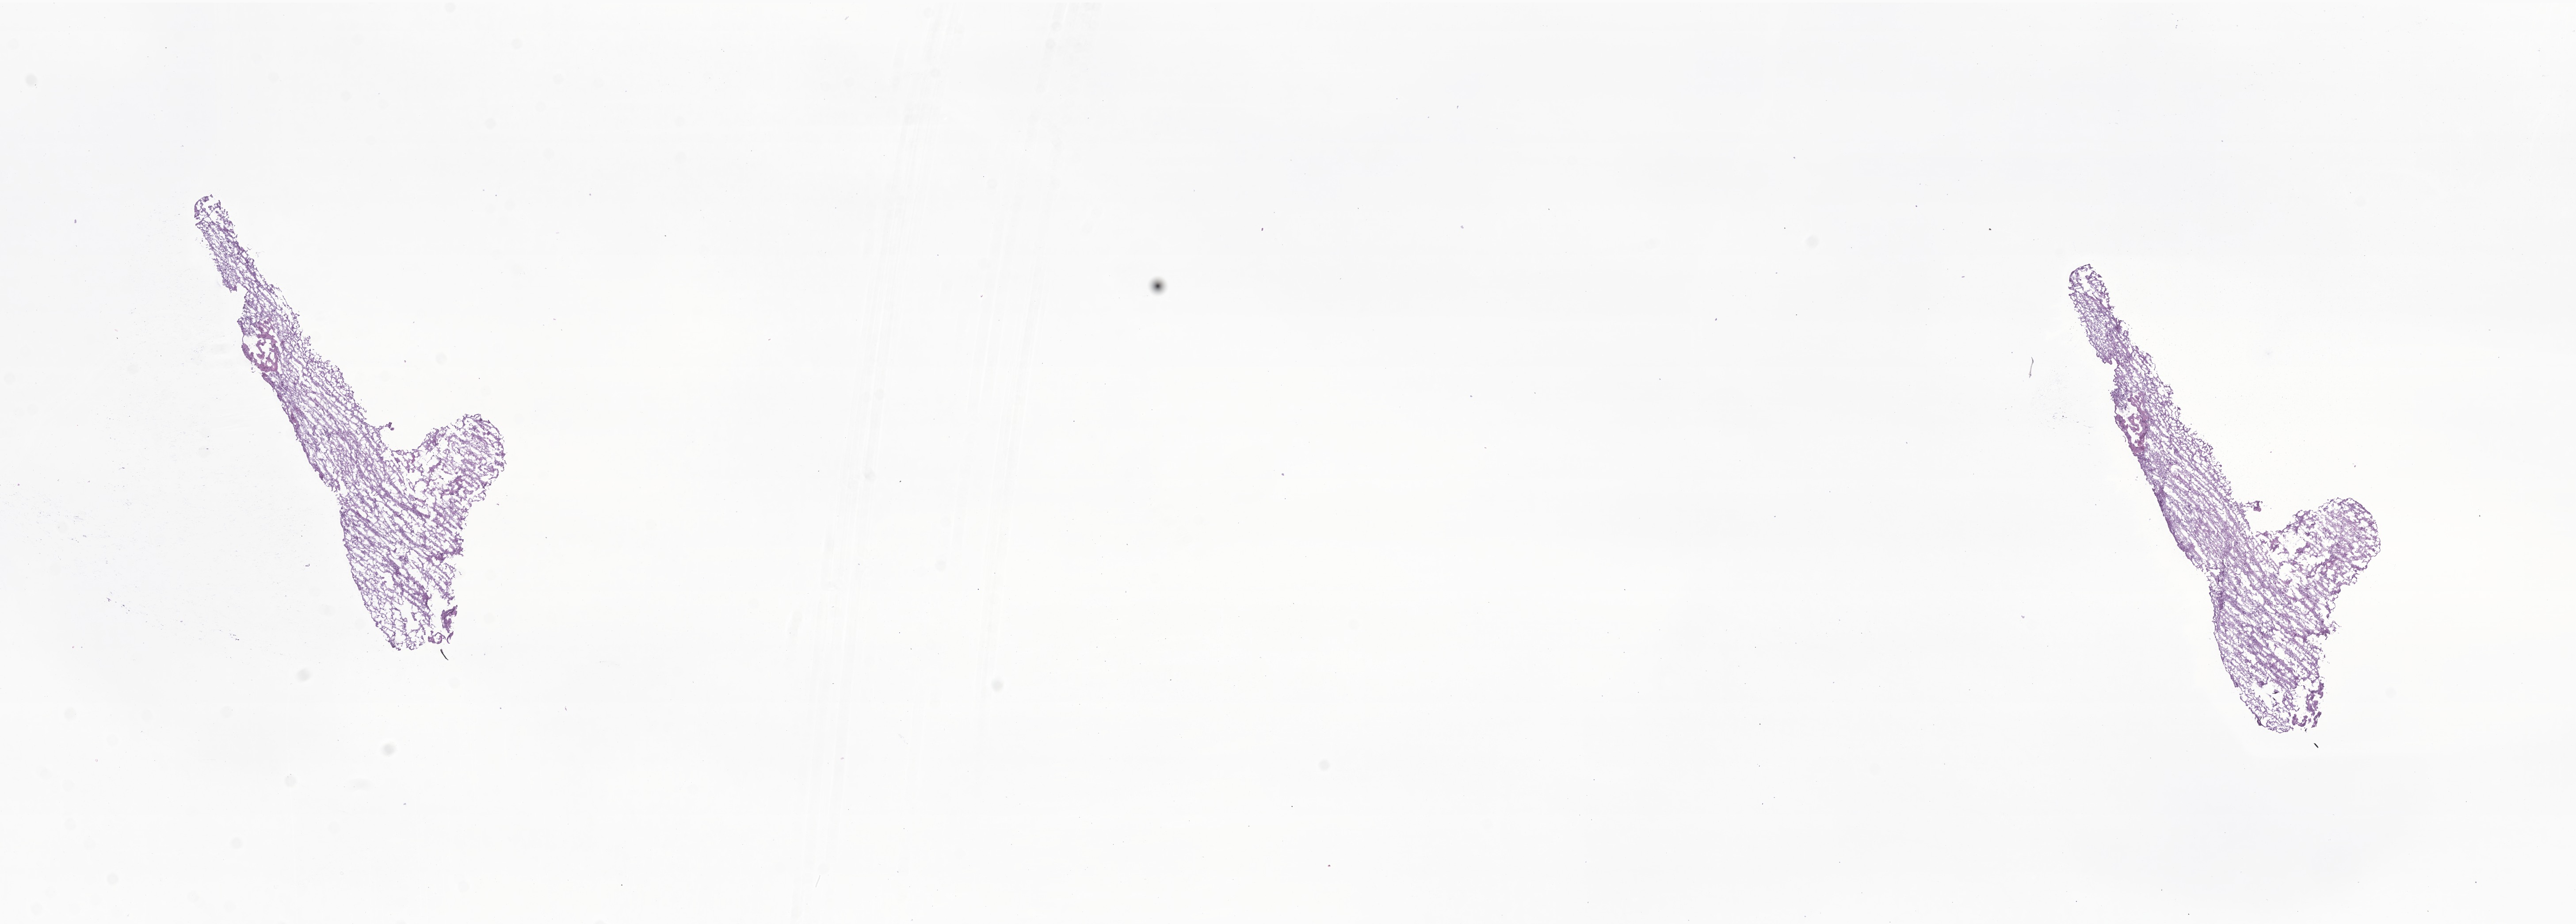
Digitized hematoxylin and eosin (H&E)-stained section of tumor tissue from the cerebellum — a low-resolution overview of the entire scanned area, about 24.6 x 8.8 mm. Frozen section (OCT-embedded). Patient: female, age 202 months (16 years 10 months).
Diagnosis: Pilocytic astrocytoma.